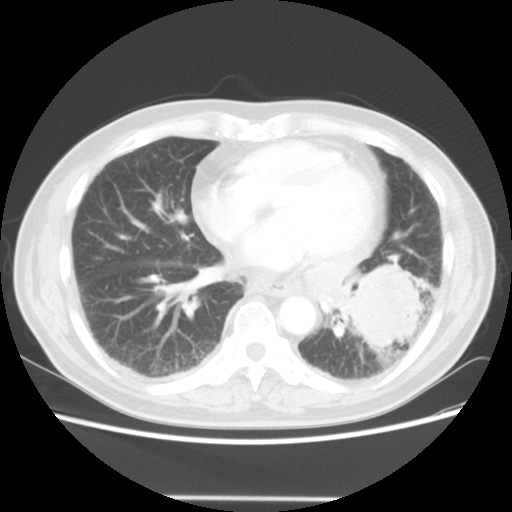
Chest CT, one axial slice. Position 19 of 56 along the scan axis. Reconstruction kernel STANDARD. 140 kVp. Lung window (W 1500 / L -600 HU). 5 mm slice thickness. 512 × 512 image matrix, field of view 360 × 360 mm. Male patient, age 66 years. From the clinical record (not read from this slice): clinical TNM (as recorded): T4 N3 M0; histopathological grade: G3.
Annotated regions visible in this slice (rectangle marked by the reading radiologist):
- lung tumour (recorded histology: small cell carcinoma): bounding box <339,262,433,356> (left, top, right, bottom; pixels)